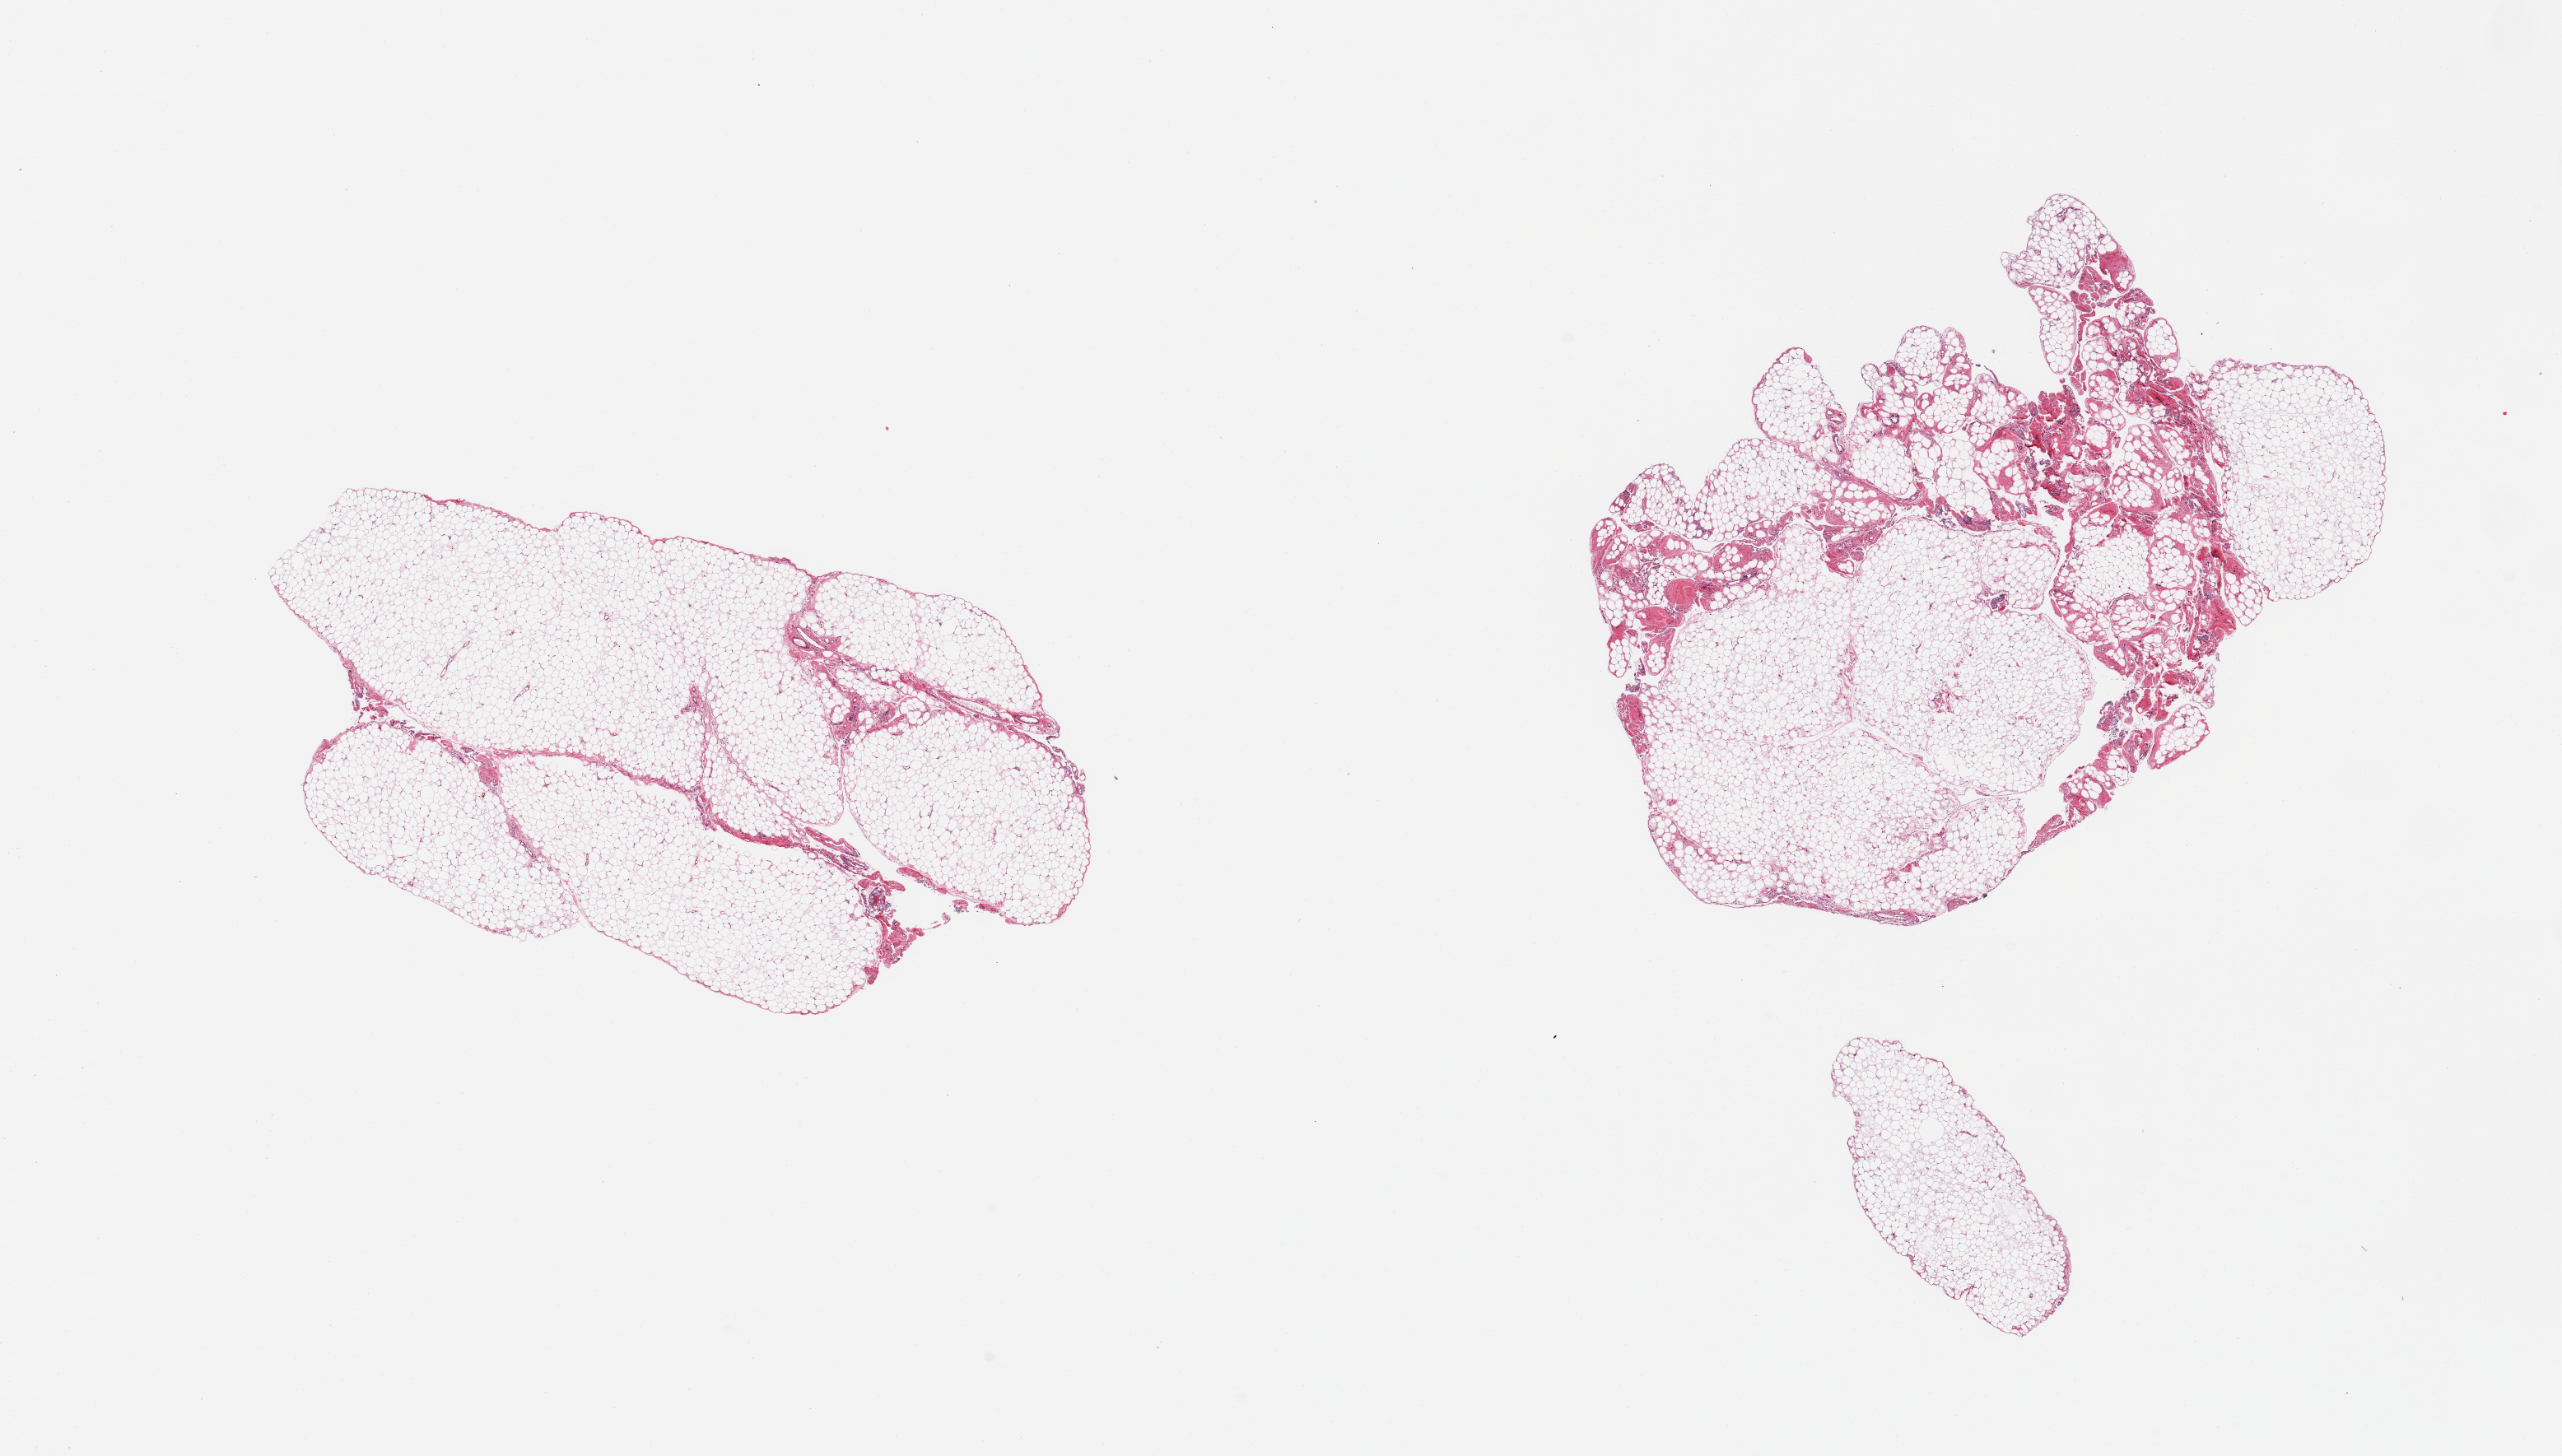
Haematoxylin and eosin whole-slide image — whole scanned area (about 24.6 x 14.0 mm) shown as a low-resolution overview. PAXgene-fixed paraffin-embedded (PFPE) section. Target tissue: omentum. Donor tissue sample. Donor: male.
Review note (as recorded): 2 pieces; 2 & 10% fibrous content.